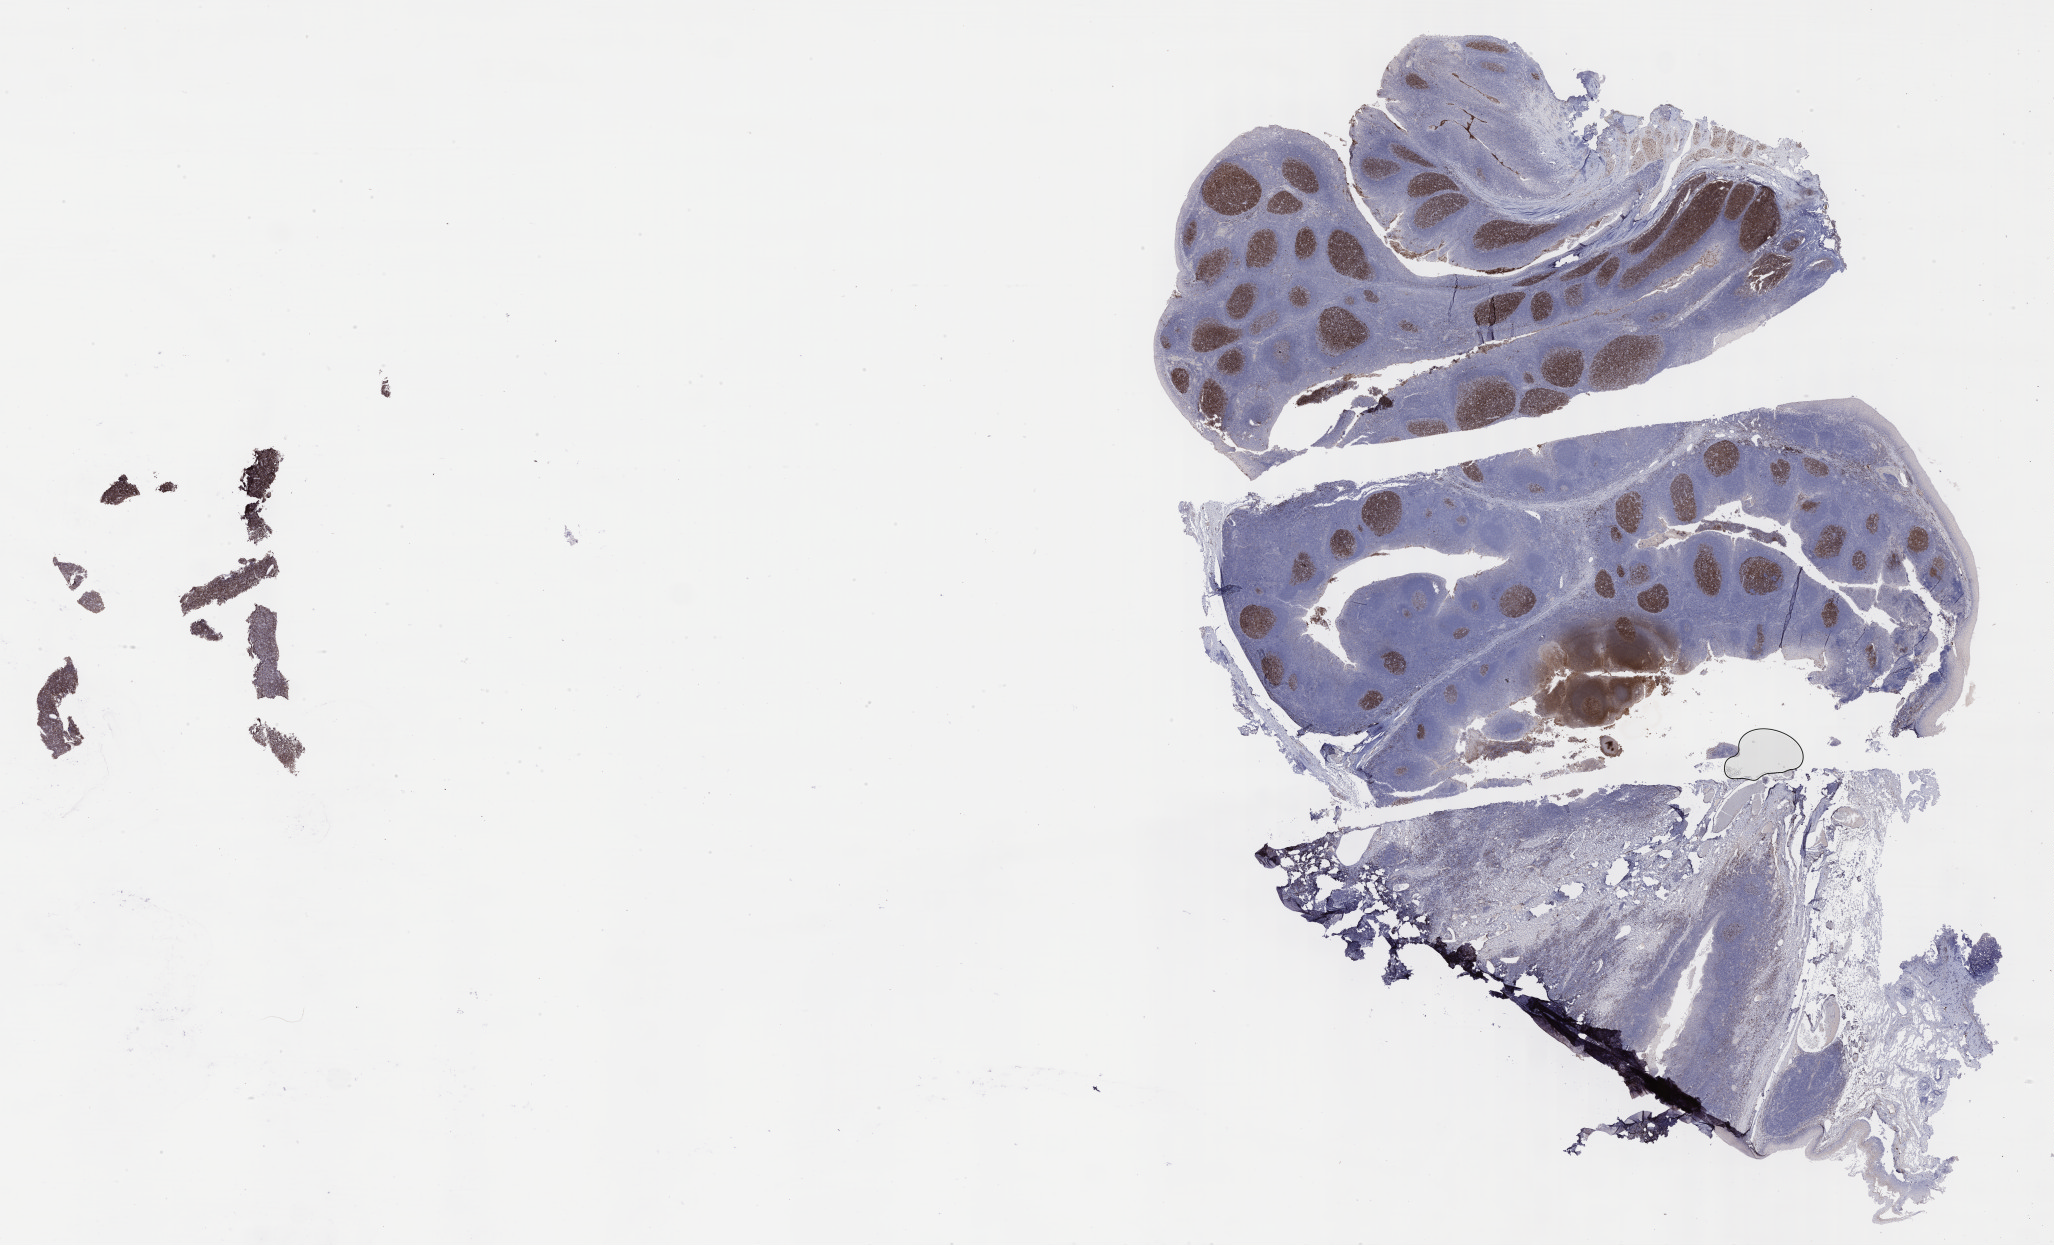
IHC for CD10, whole-slide image, shown as a low-resolution overview of the whole scanned area (about 33.2 x 20.1 mm); tumor tissue; site: peritoneum. Female patient; age at initial diagnosis 6 years.
Histologic diagnosis: Burkitt lymphoma, NOS.